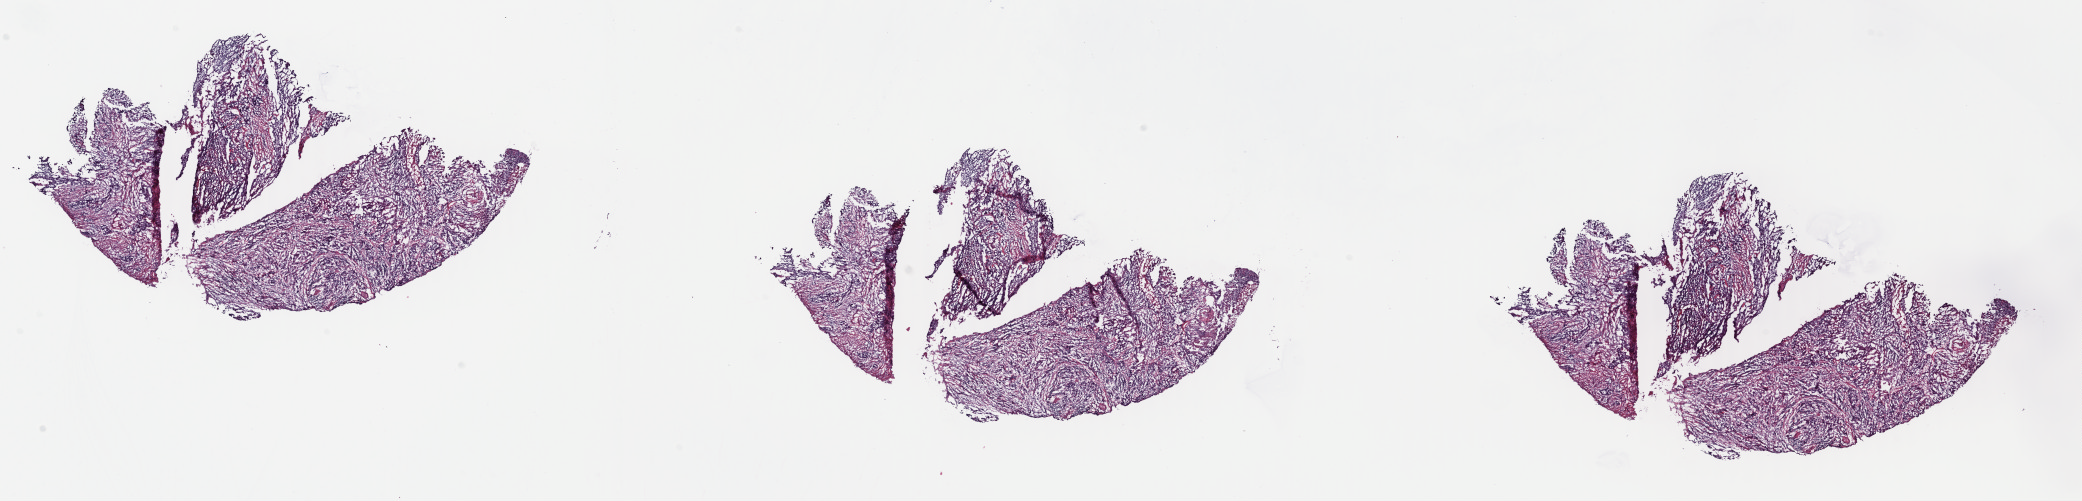
Hematoxylin and eosin (H&E) stained whole-slide image — whole scanned area (about 32.7 x 7.9 mm) shown as a low-resolution overview. Frozen section from the top of the tissue portion. Primary tumour sample from the head and neck. Male, age 72 years at initial diagnosis. Histologic grade: G3 (poorly differentiated). Pathologist review of this section (percent, as recorded): tumour cells 70%, tumour nuclei 80%, normal cells 0%, stromal cells 30%, necrosis 0%. Infiltration values recorded for this section: lymphocyte infiltration 0%, monocyte infiltration 0%, neutrophil infiltration 0%.
* histologic diagnosis: Squamous cell carcinoma, NOS (larynx, NOS)